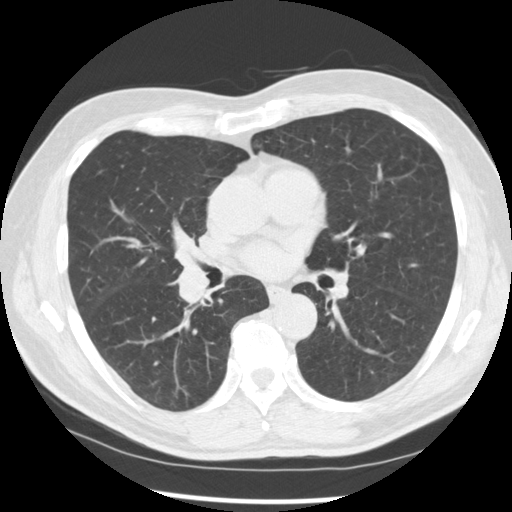
Low-dose screening chest CT, one axial slice; position 150 of 277 along the scan axis; lung window (W 1500 / L -600 HU); 2.5 mm slice thickness; 512 × 512 image matrix.
Outlined on this slice (expert manual segmentation):
- lesion 1 (tumor, middle lobe of right lung): bounding box <174,262,210,307> (left, top, right, bottom; pixels)